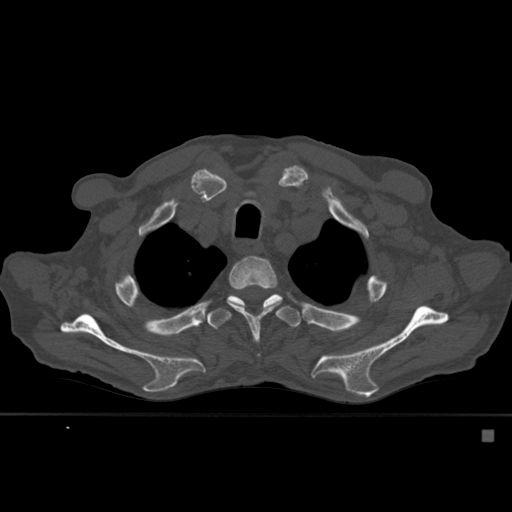
CT including the spine, one axial slice. Bone window (W 1800 / L 400 HU). 512 × 512 image matrix, field of view 373 × 373 mm. Patient: male, 78 years. Case-level facts recorded for this patient, not image findings: primary cancer: prostate.
Outlined on this slice (semi-automatically segmented with operator editing):
- T3 vertebra: bounding box (x1, y1, x2, y2) in pixels: (227, 256, 278, 340)
- T4 vertebra: (207, 286, 302, 329)